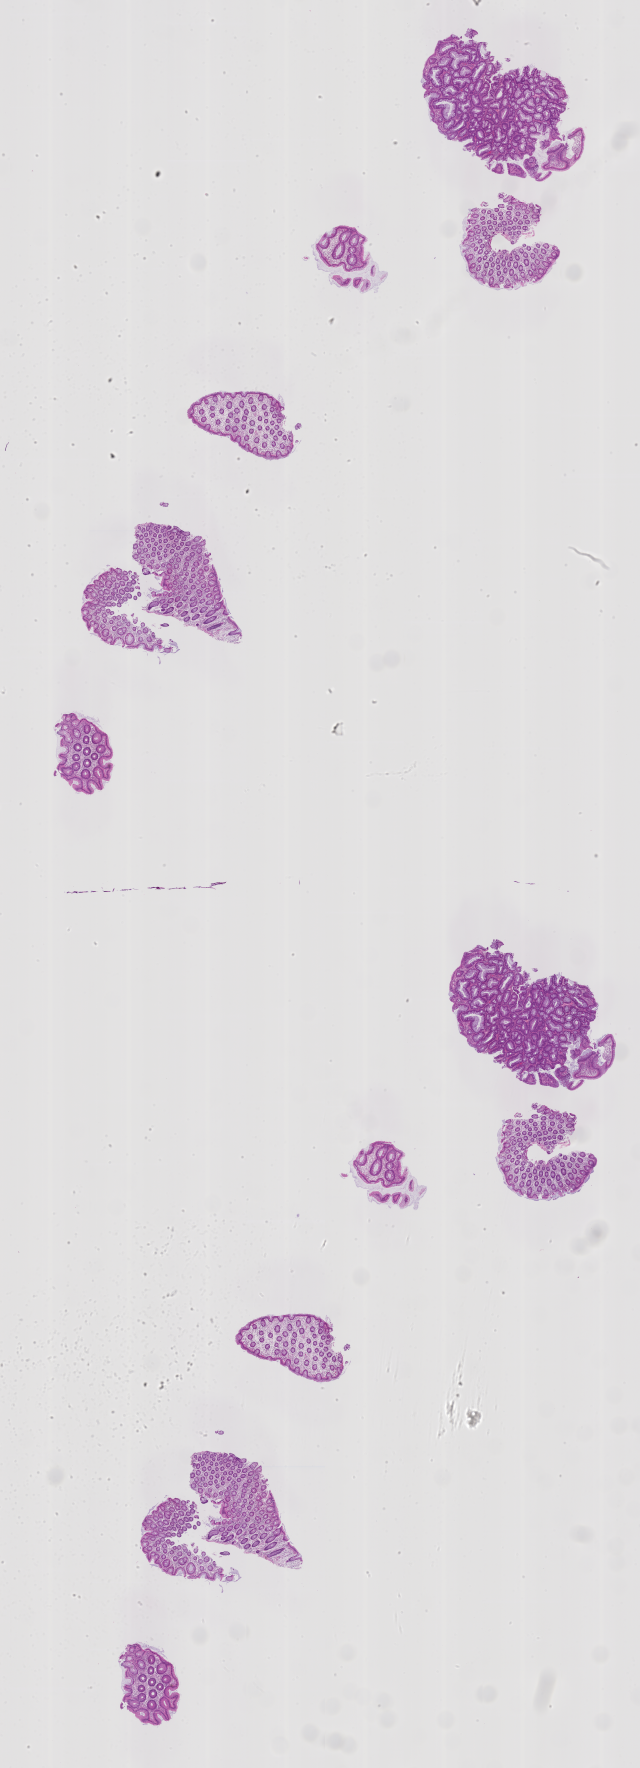
Whole-slide image, hematoxylin and eosin (H&E) stain: colon biopsy — shown as a low-resolution overview of the whole scanned area (about 10.2 x 28.3 mm); formalin-fixed, paraffin-embedded (FFPE) tissue; site: transverse colon. Patient sex: male.
Lesion category (as recorded): premalignant.